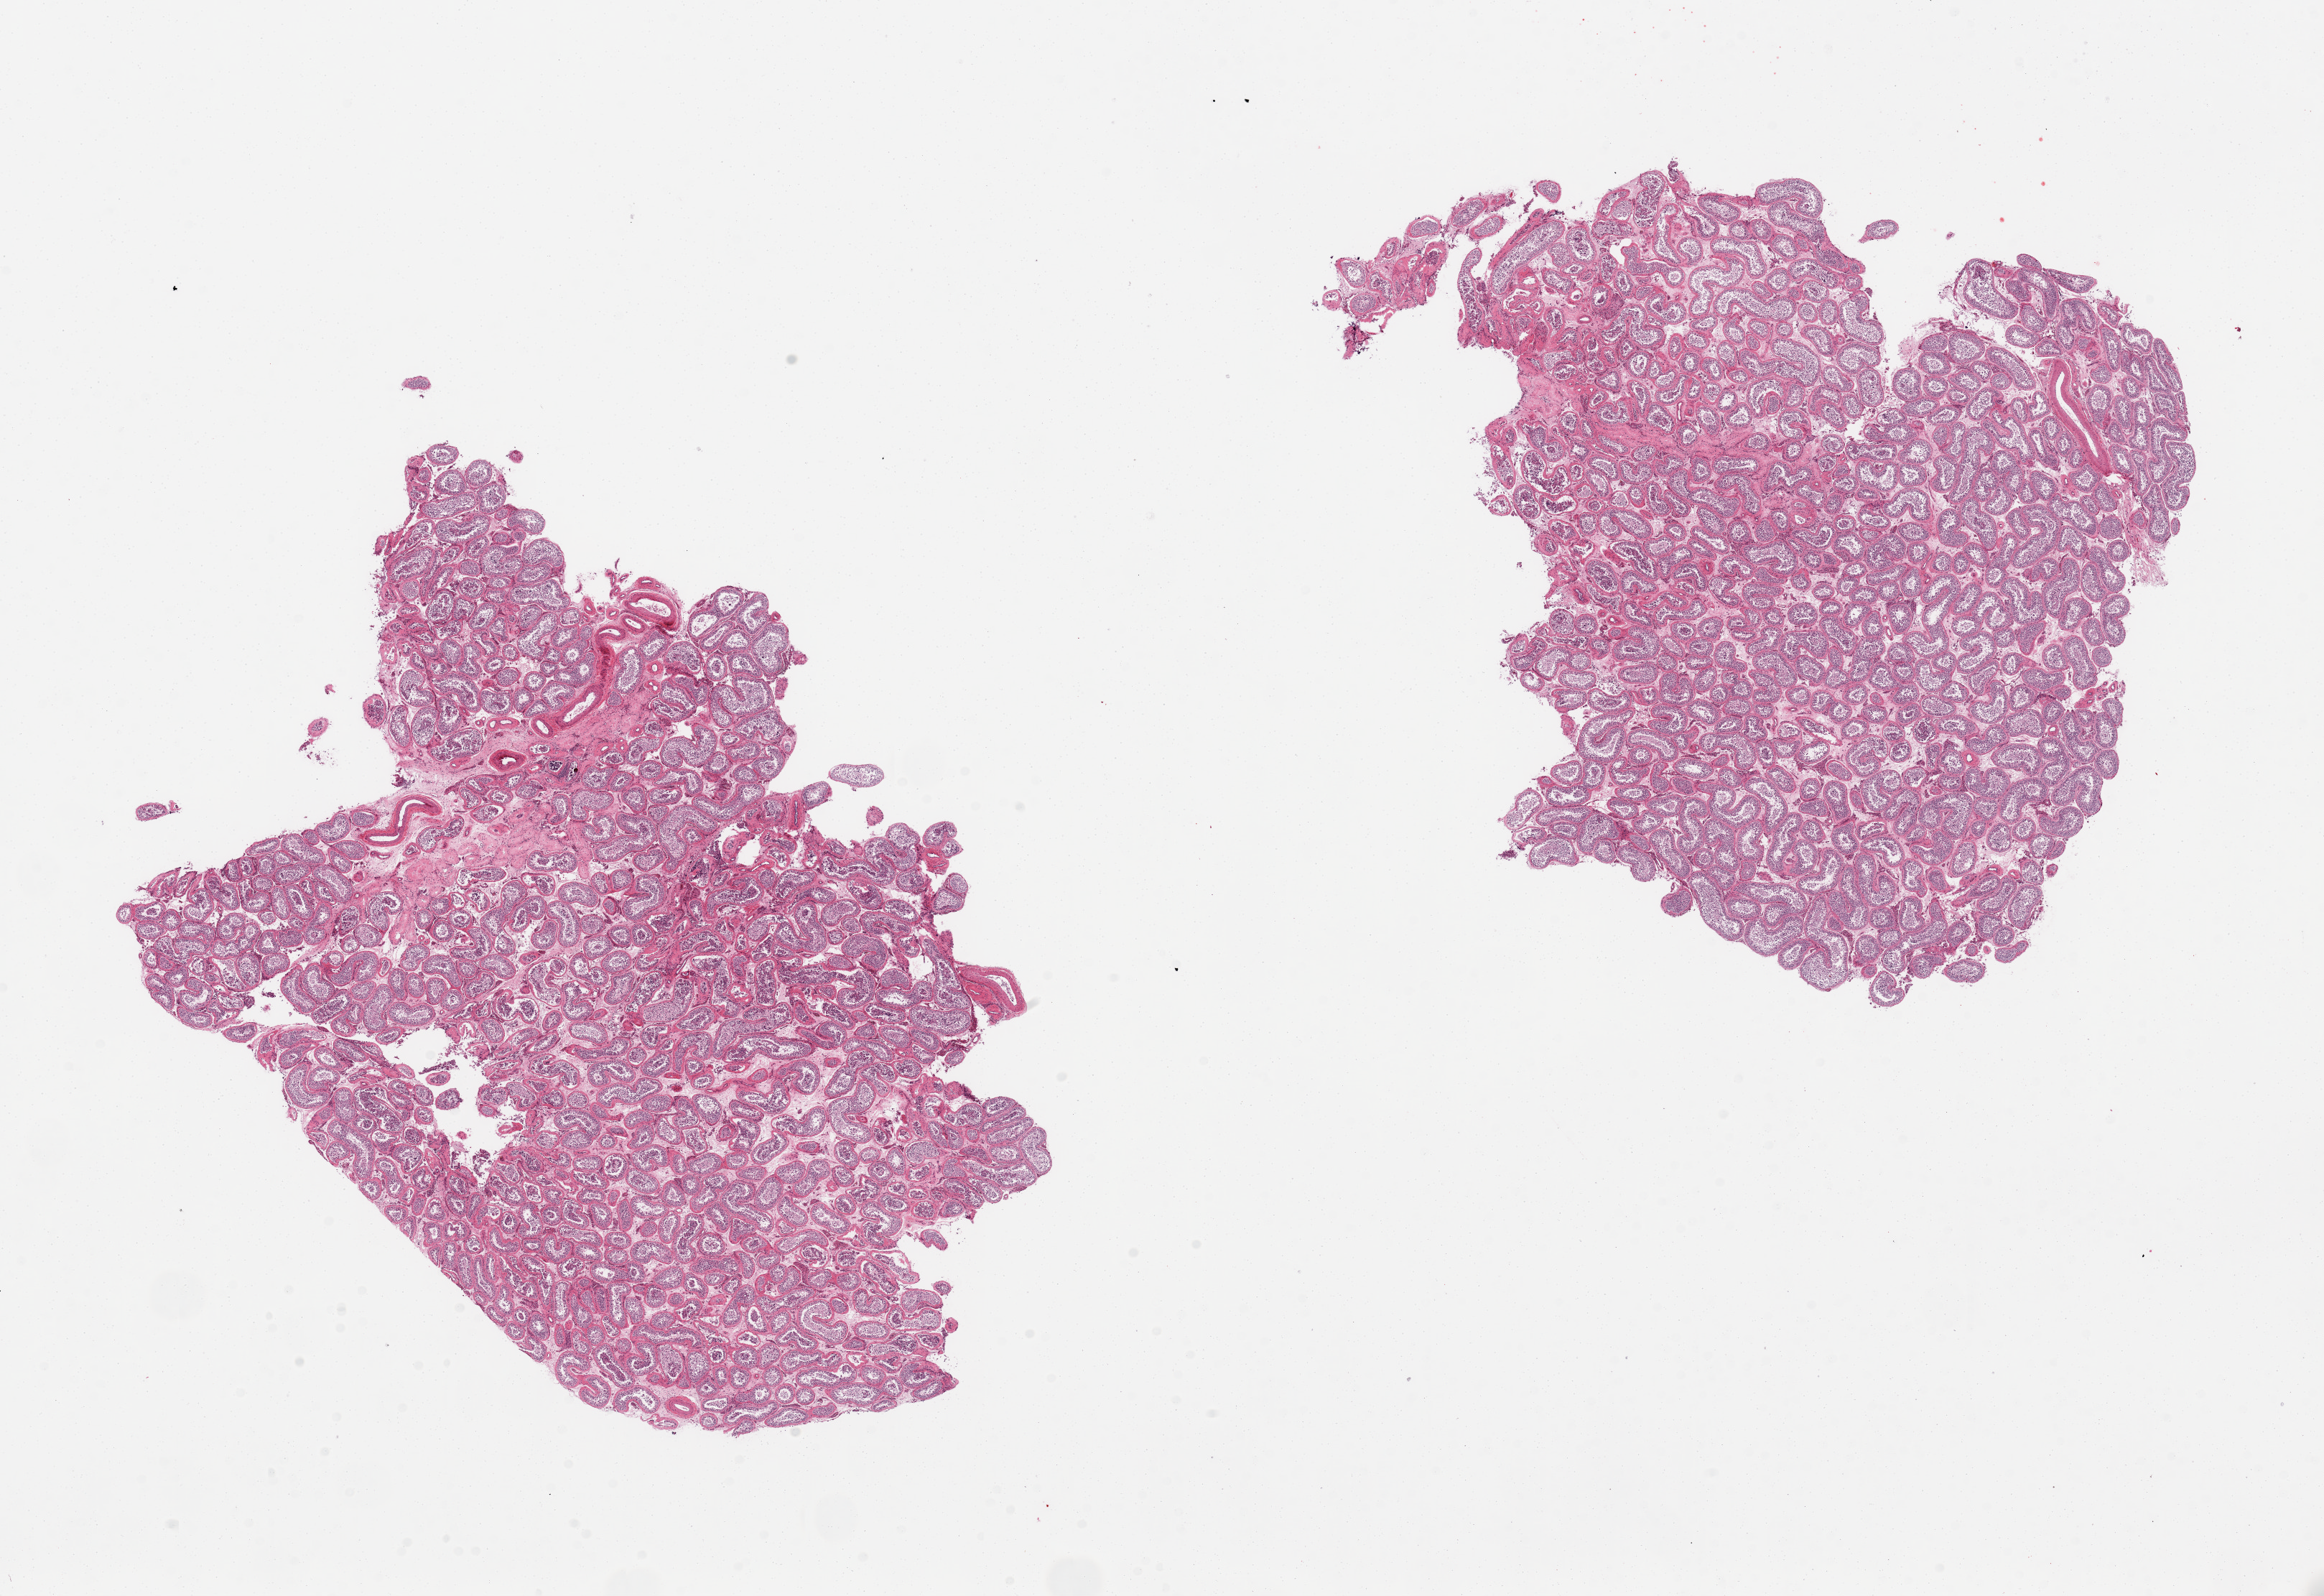
Digitized haematoxylin and eosin-stained section — shown as a low-resolution overview of the whole scanned area (about 25.6 x 17.6 mm, slide scanned at 20x). PAXgene-fixed, paraffin-embedded tissue. Target tissue: testis. Donor tissue sample. Donor: male.
Reviewer comment on this tissue sample: 2 pieces; spermatogenesis.